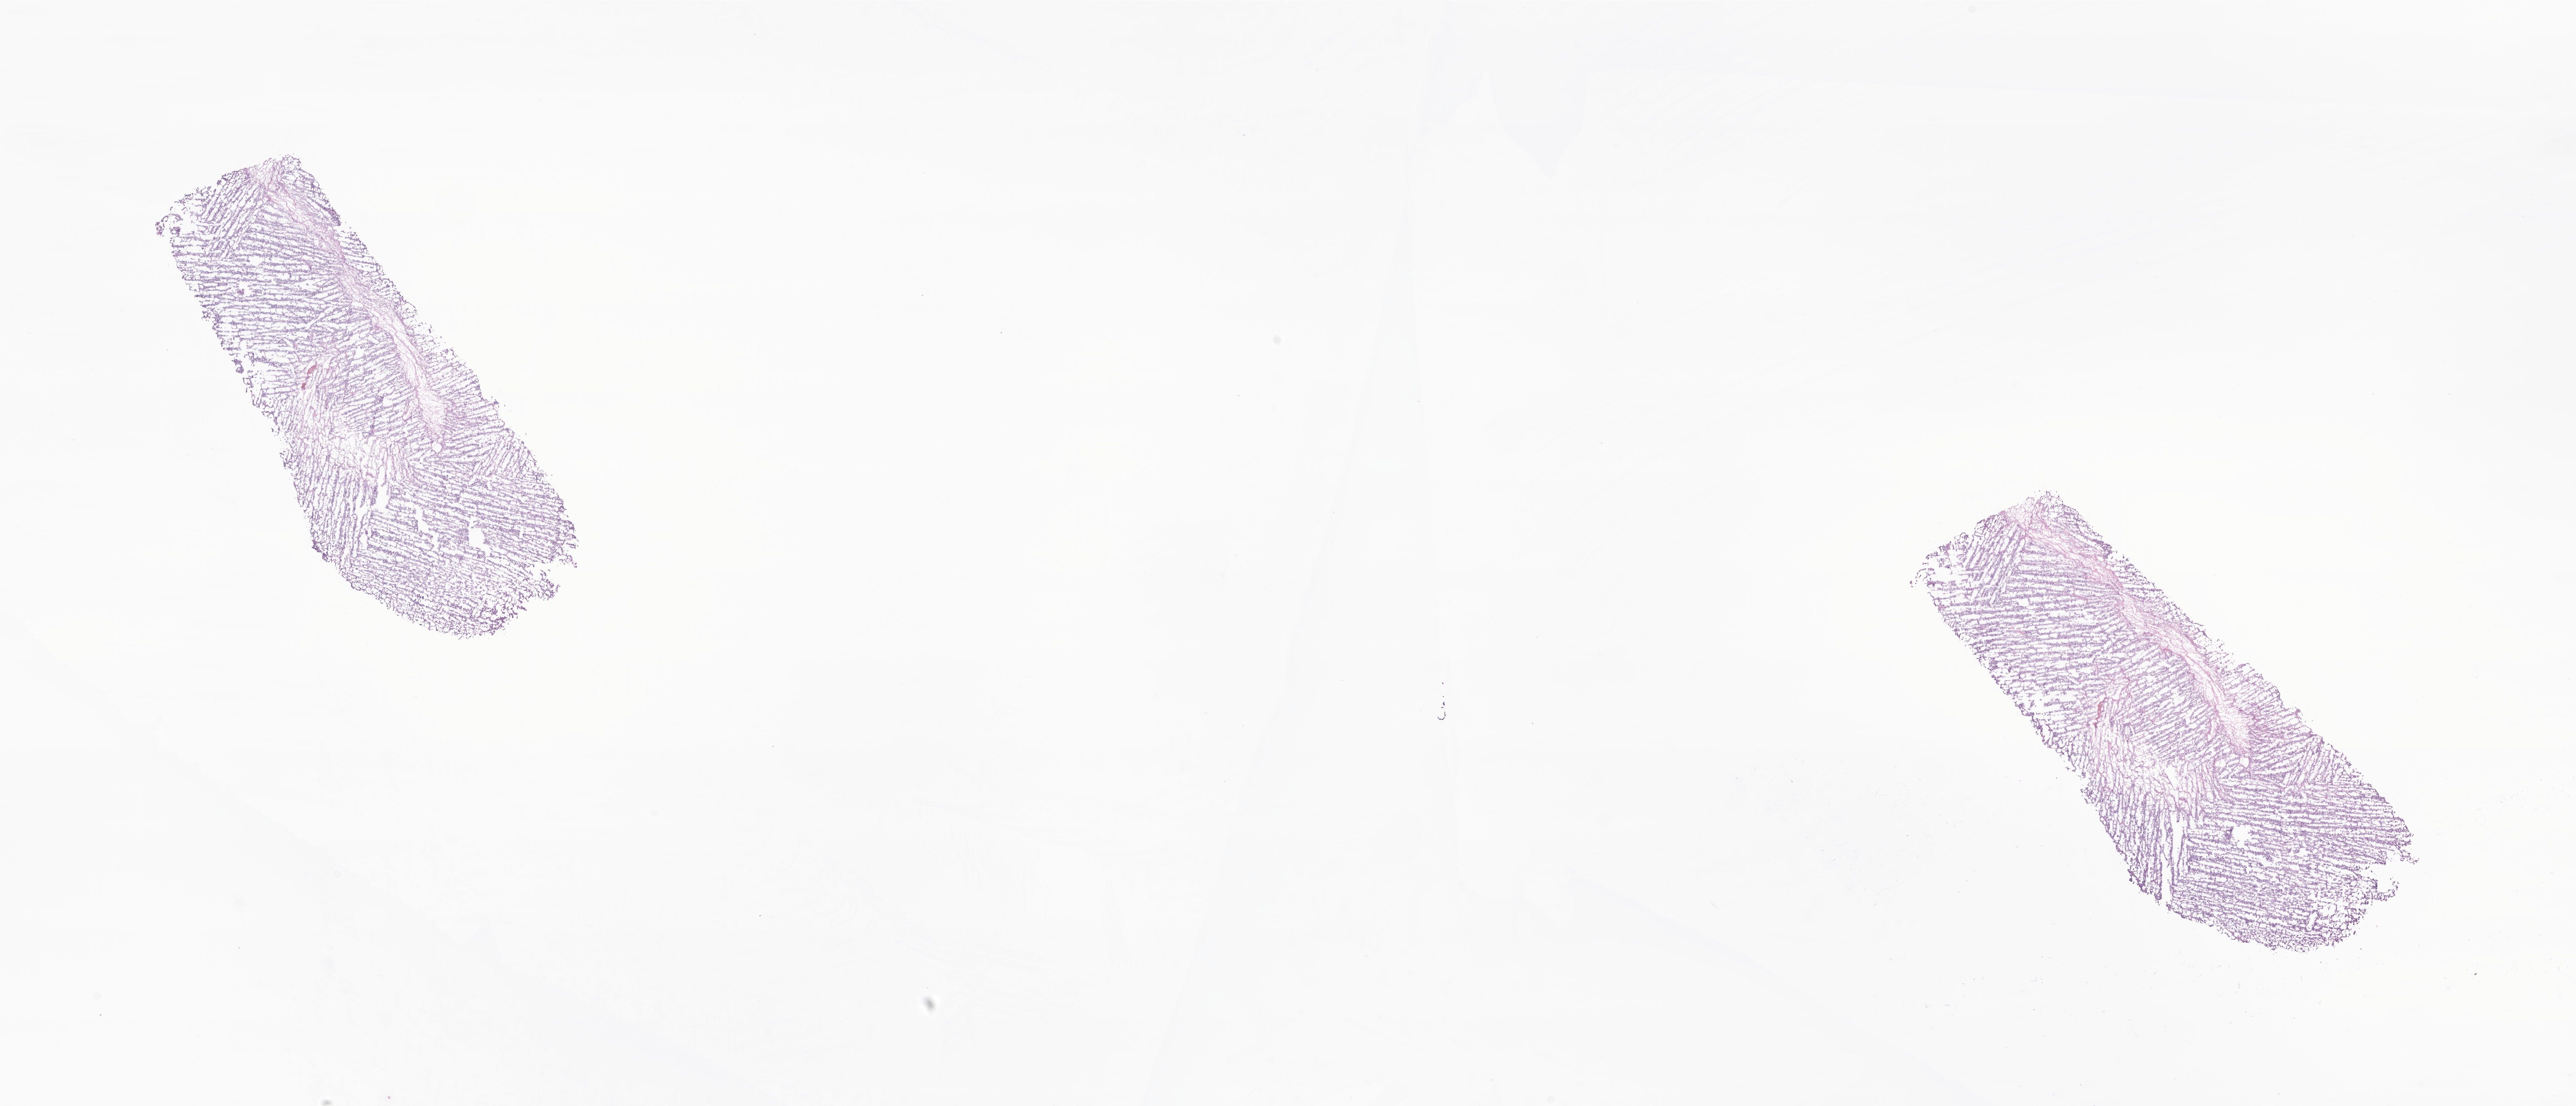
Digitized haematoxylin and eosin-stained section of tumor tissue from the brain — a low-resolution overview of the entire scanned area, about 30.8 x 13.2 mm. Frozen section. Female patient, age 114 months (9 years 6 months).
Recorded diagnosis: Neoplasm, uncertain whether benign or malignant.